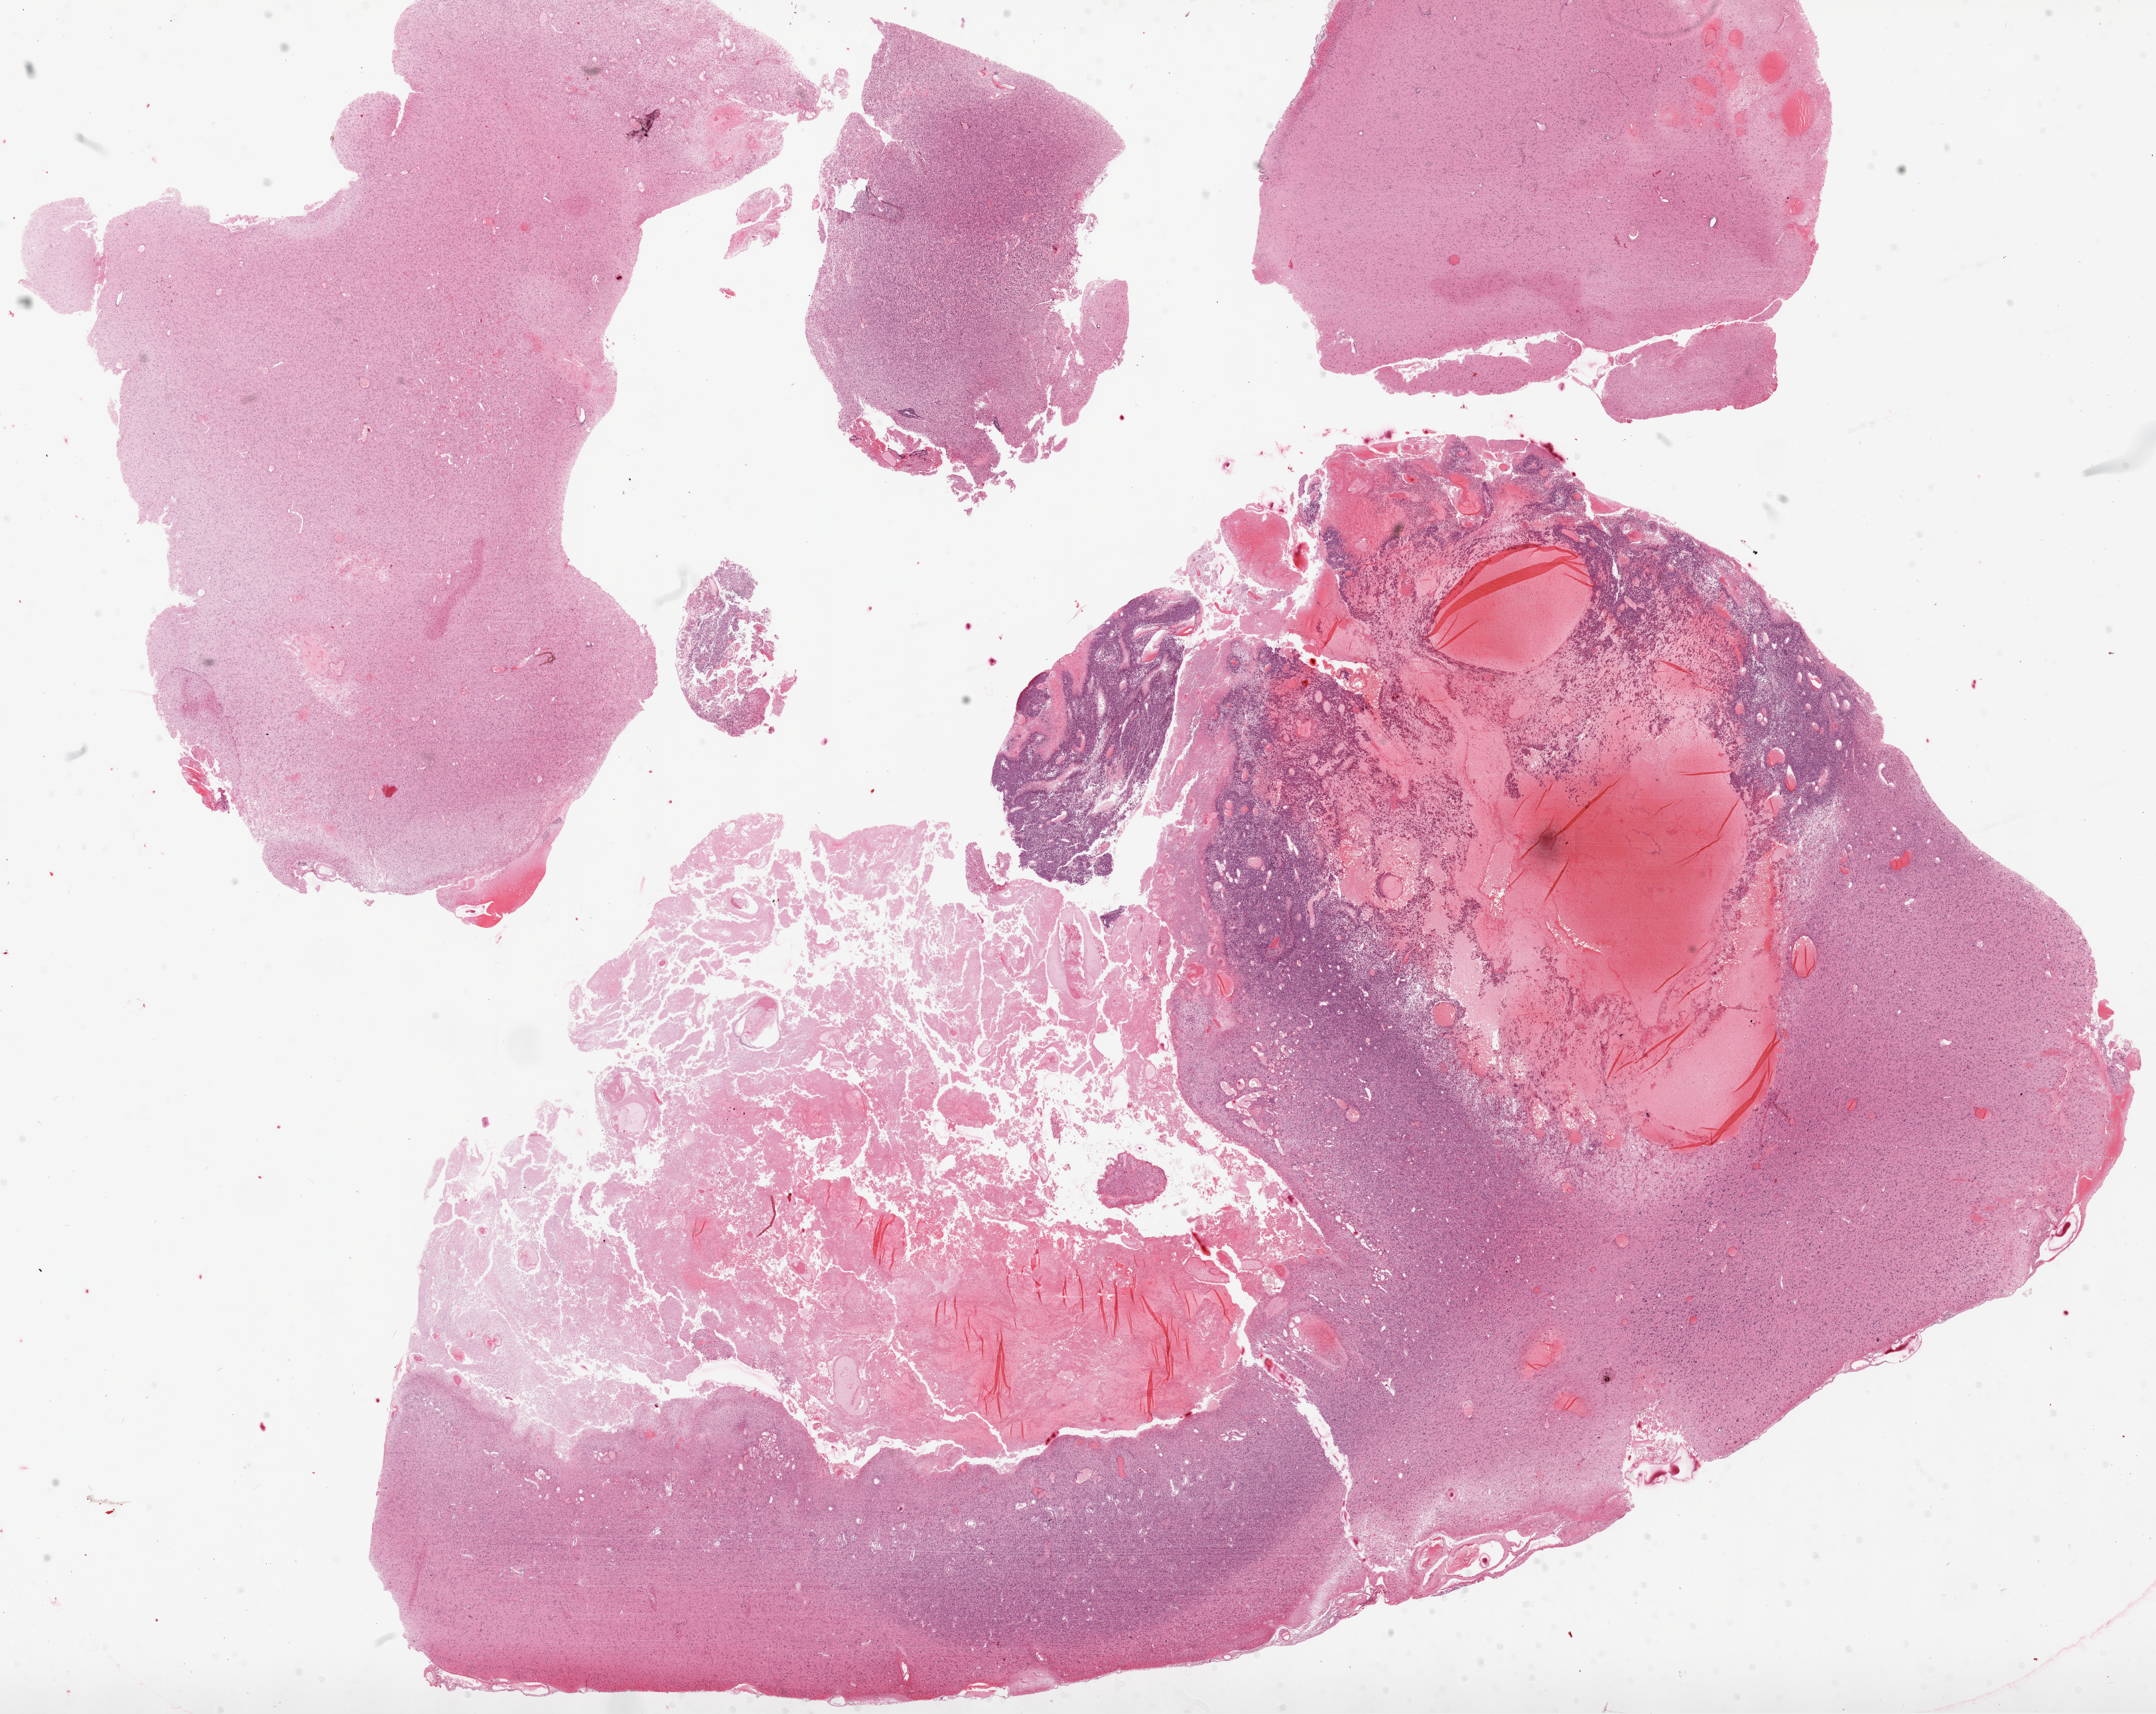
Whole-slide histology image, H&E-stained — whole scanned area (about 26.1 x 20.7 mm) shown as a low-resolution overview; FFPE section; brain, primary tumour sample. Female patient; age at initial diagnosis 33 years.
Pathologic diagnosis: Glioblastoma.